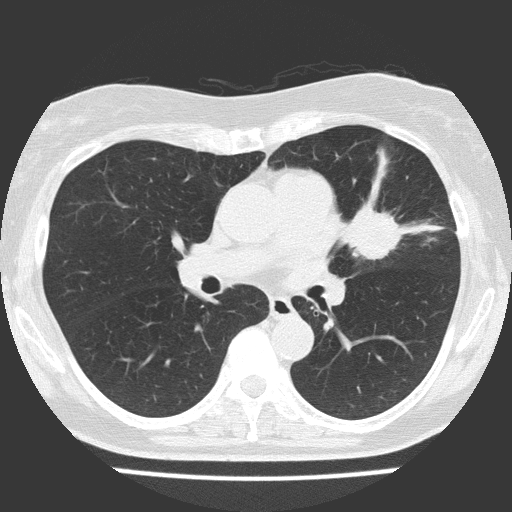
Low-dose screening chest CT, one axial slice; slice 82 of 151 in the series (ordered by position); reconstruction kernel FC51; 120 kVp; lung window (W 1500 / L -600 HU); 2 mm slice thickness; 512 × 512 image matrix.
Annotated regions visible in this slice (expert manual segmentation):
- lesion 1 (tumor, upper lobe of left lung): box from (x=341, y=201) to (x=404, y=260) px